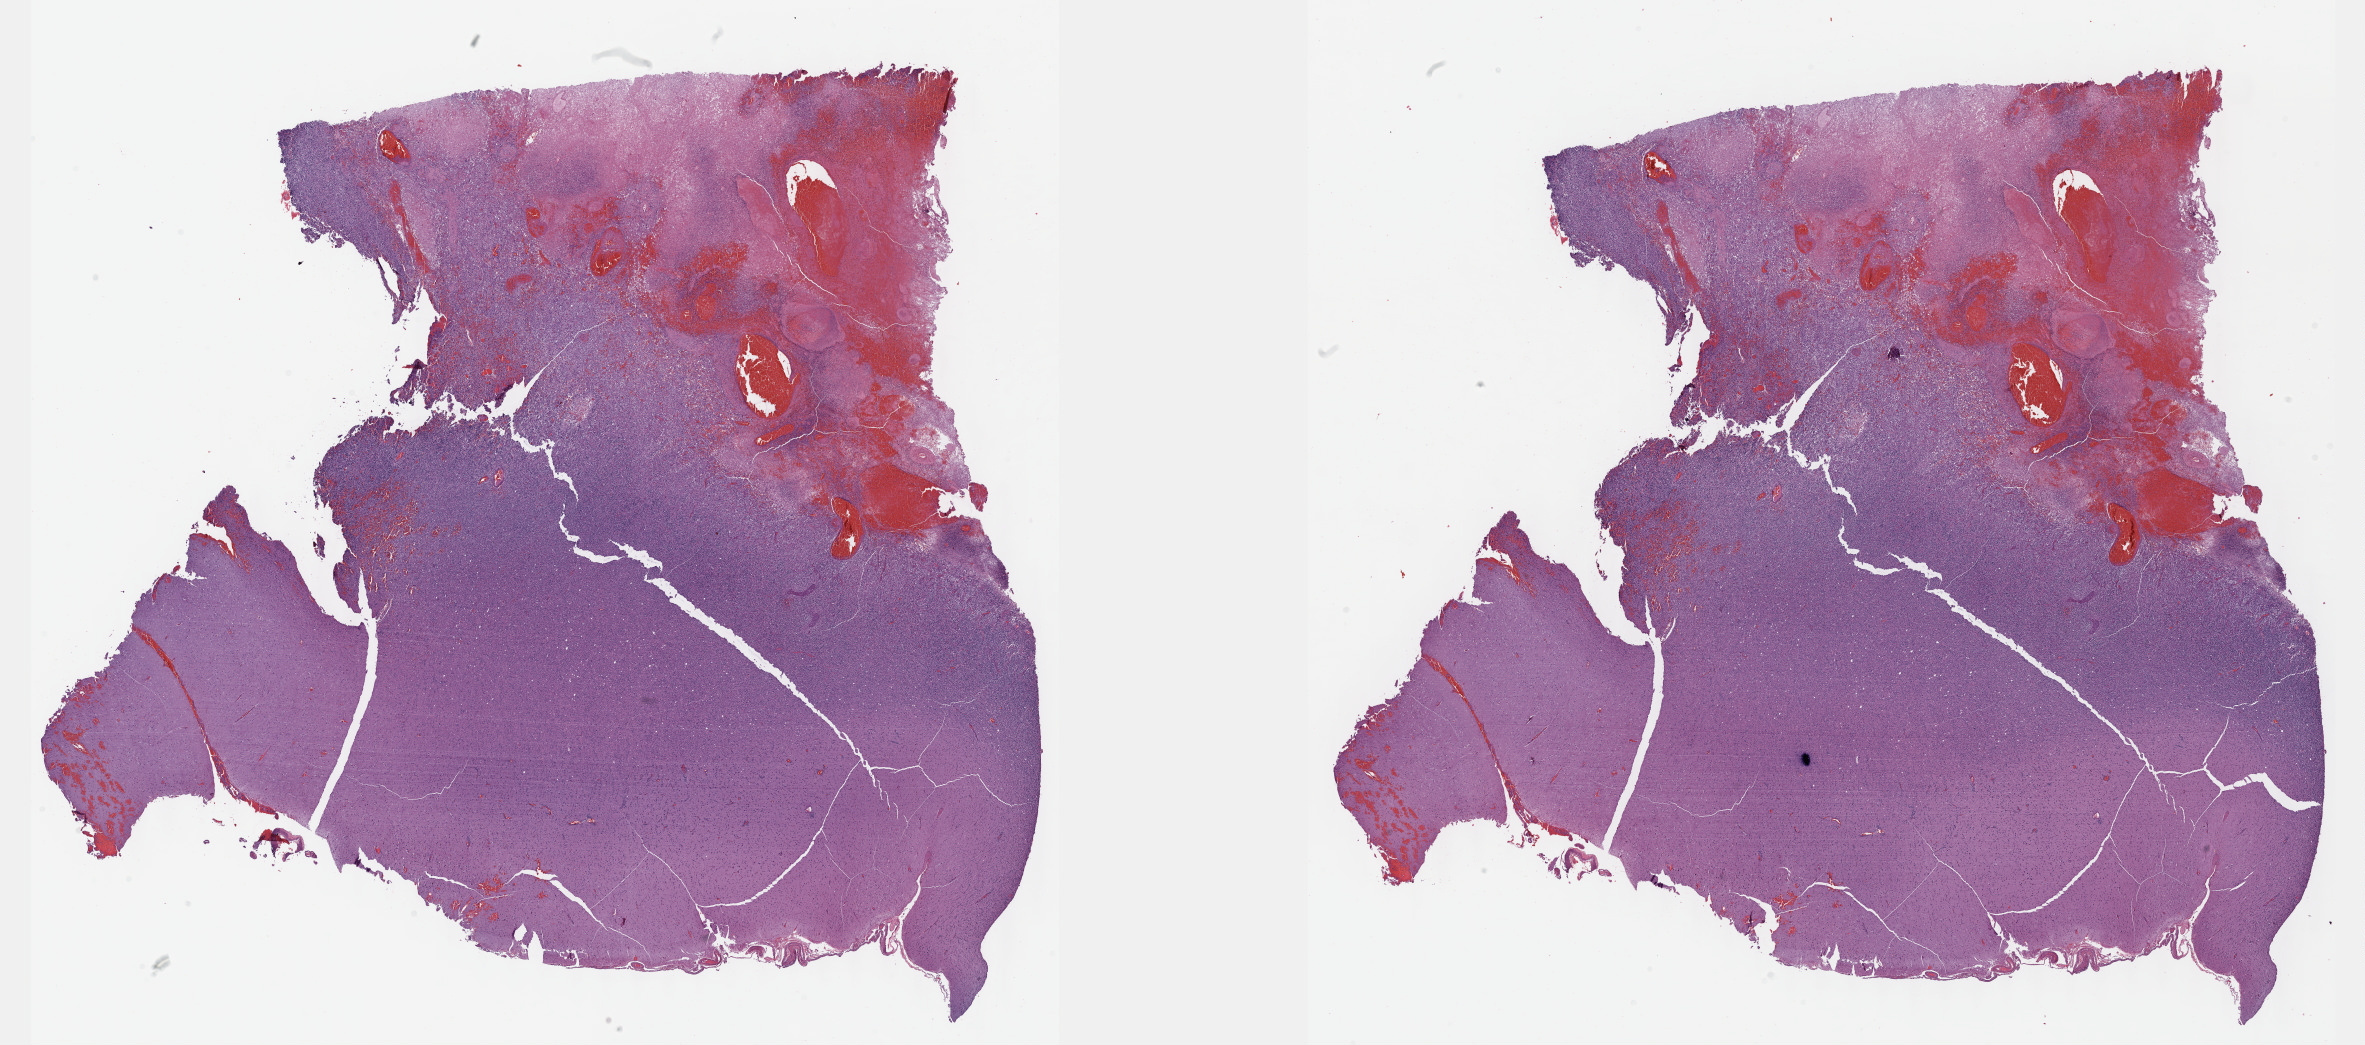
Digitized Hematoxylin and eosin (H&E) stained tissue section (whole slide) — a low-resolution overview of the entire scanned area, about 38.2 x 16.9 mm; formalin-fixed paraffin-embedded (FFPE) diagnostic section; primary tumour sample from the brain. Male patient; age at initial diagnosis 40 years.
Histologic diagnosis: Glioblastoma.